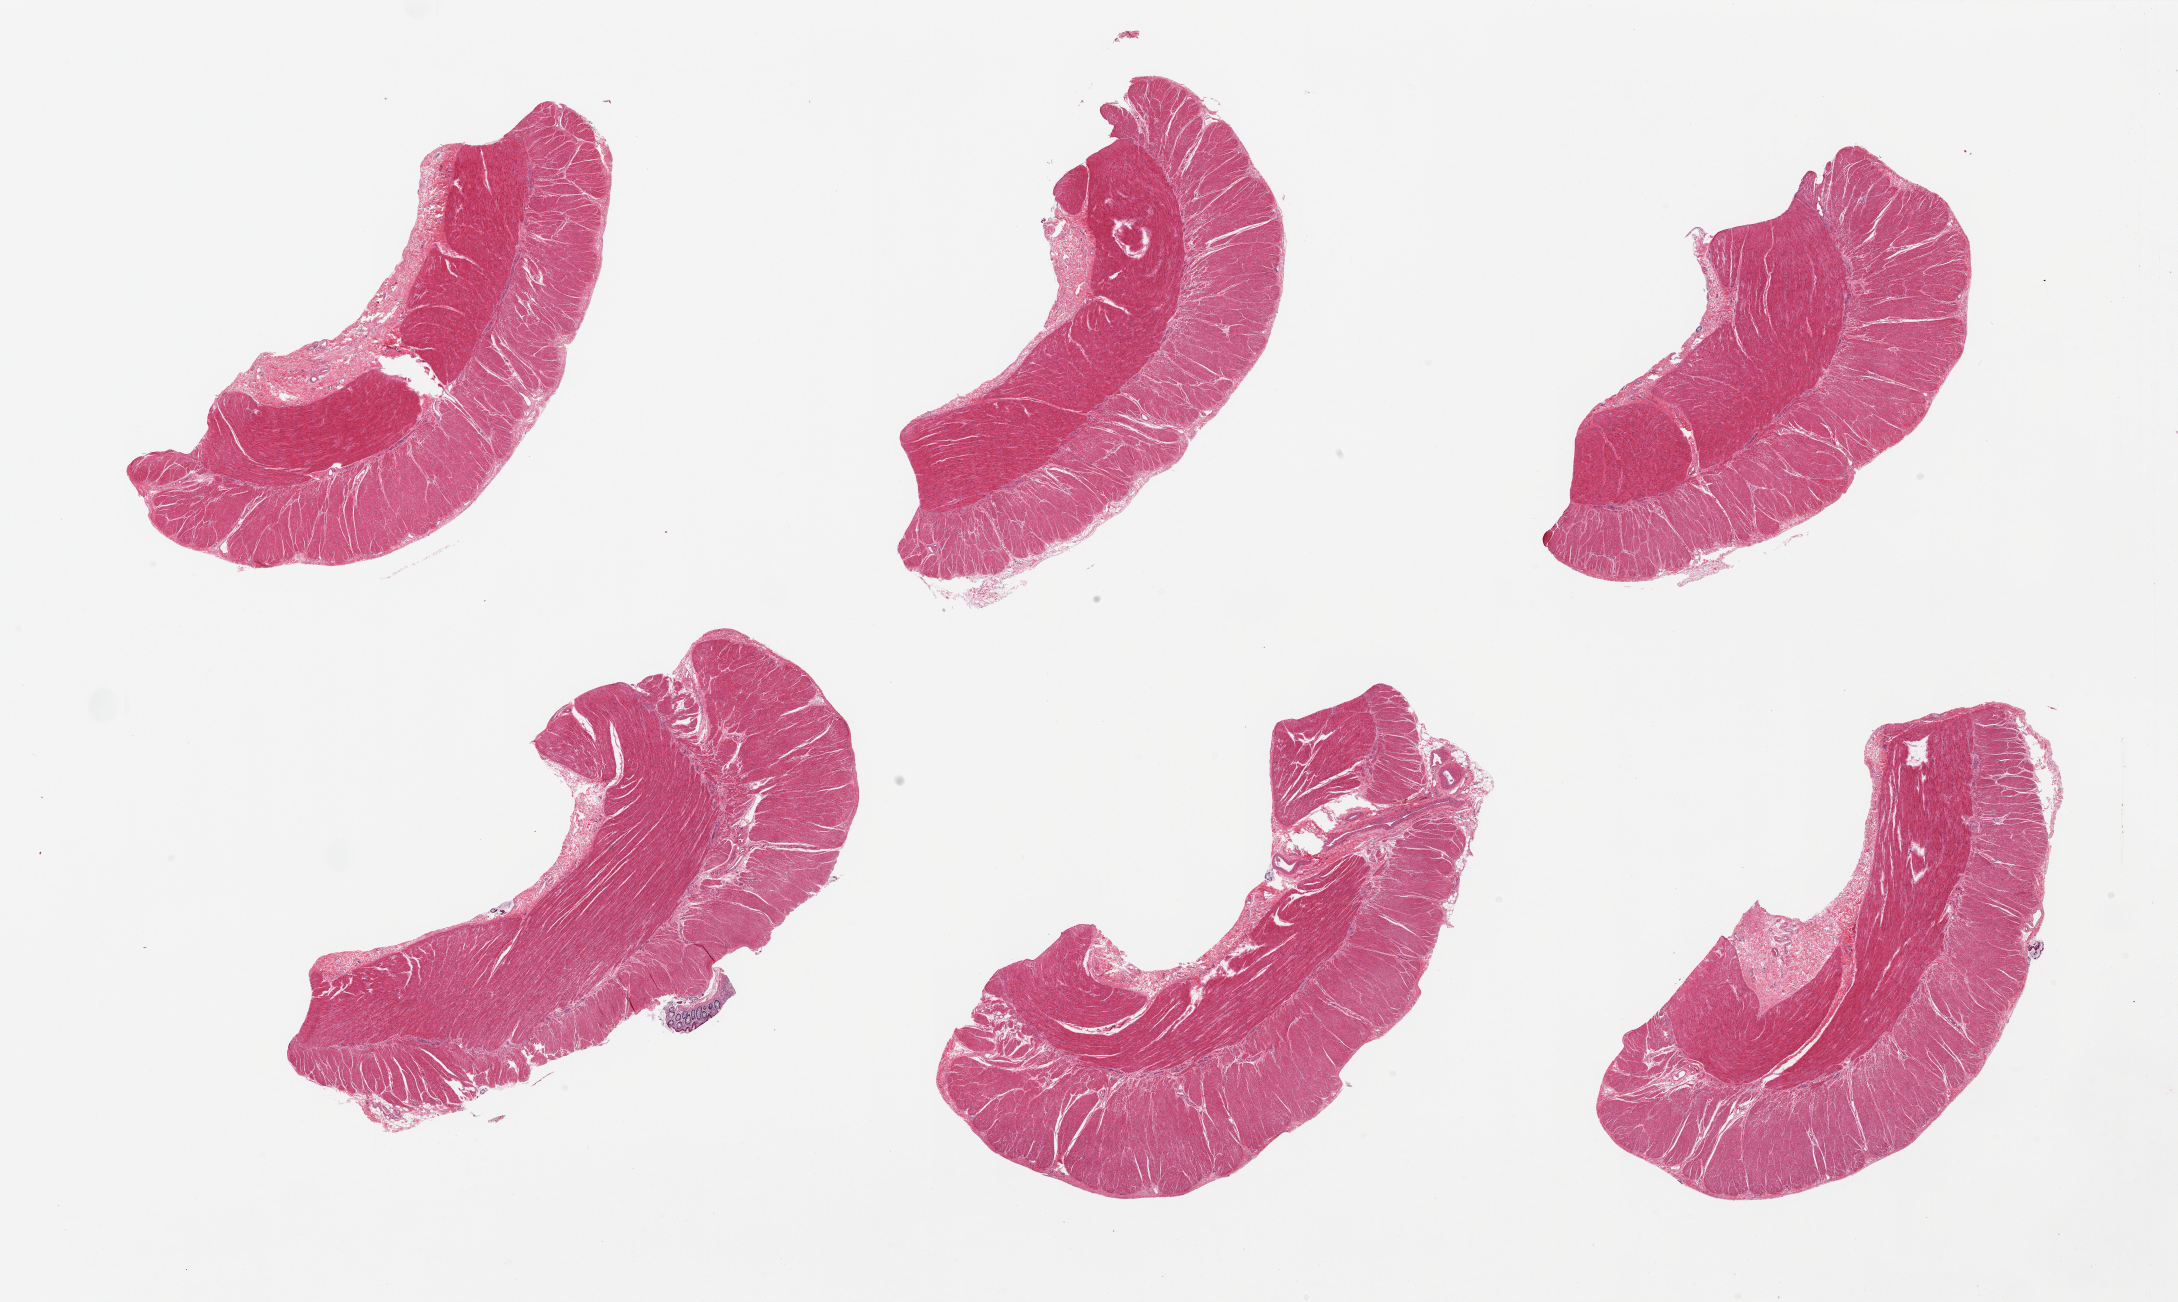
Whole-slide image, hematoxylin and eosin (H&E) stain, brightfield, low-resolution overview of the scanned area, about 34.5 x 20.6 mm. PAXgene-fixed paraffin-embedded (PFPE) section. Sampled site (target tissue): sigmoid colon. Donor tissue sample. Donor sex: female.
Review note (as recorded): 6 pieces, all muscularis.